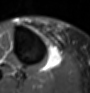
MRI of an extremity soft-tissue mass, one axial slice. Slice 37 of 60 in the series (ordered by position). STIR. MR volume resampled by the dataset authors to the PET/CT grid (not the native acquisition matrix). 90 × 93 image matrix, field of view 88 × 91 mm. Female patient. Case-level facts recorded for this patient, not image findings: histological type: undifferentiated – high grade; grade: high; site of the primary tumour: right thigh.
Structures marked on this image (expert contour drawn on MRI and transferred to this co-registered scan by the dataset authors):
- gross tumour volume (mass): bounding box <46,46,63,70> (left, top, right, bottom; pixels)